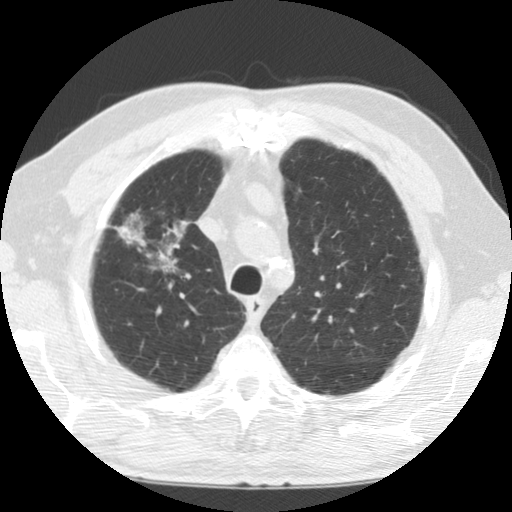
Chest CT (low-dose screening protocol), one axial image, first (baseline) screen, lung window (W 1500 / L -600 HU), 2.5 mm slice thickness, standard (soft-tissue) reconstruction kernel (STANDARD), 120 kVp, slice 22 of 124 in the series. Male participant, aged 69 years at enrolment. Former smoker at enrolment.
Expert-annotated lung lesion, bounding box [x1, y1, x2, y2] px = [102, 205, 201, 291]. No non-calcified nodule or mass ≥4 mm was recorded by the screening reader at this exam. Official screen result: negative screen, minor abnormalities not suspicious for lung cancer. Later outcome: lung cancer diagnosed 171 days after this screen — adenocarcinoma, NOS, right upper lobe, poorly differentiated (G3), stage IIIB (AJCC 6th edition), 40 mm at pathology.